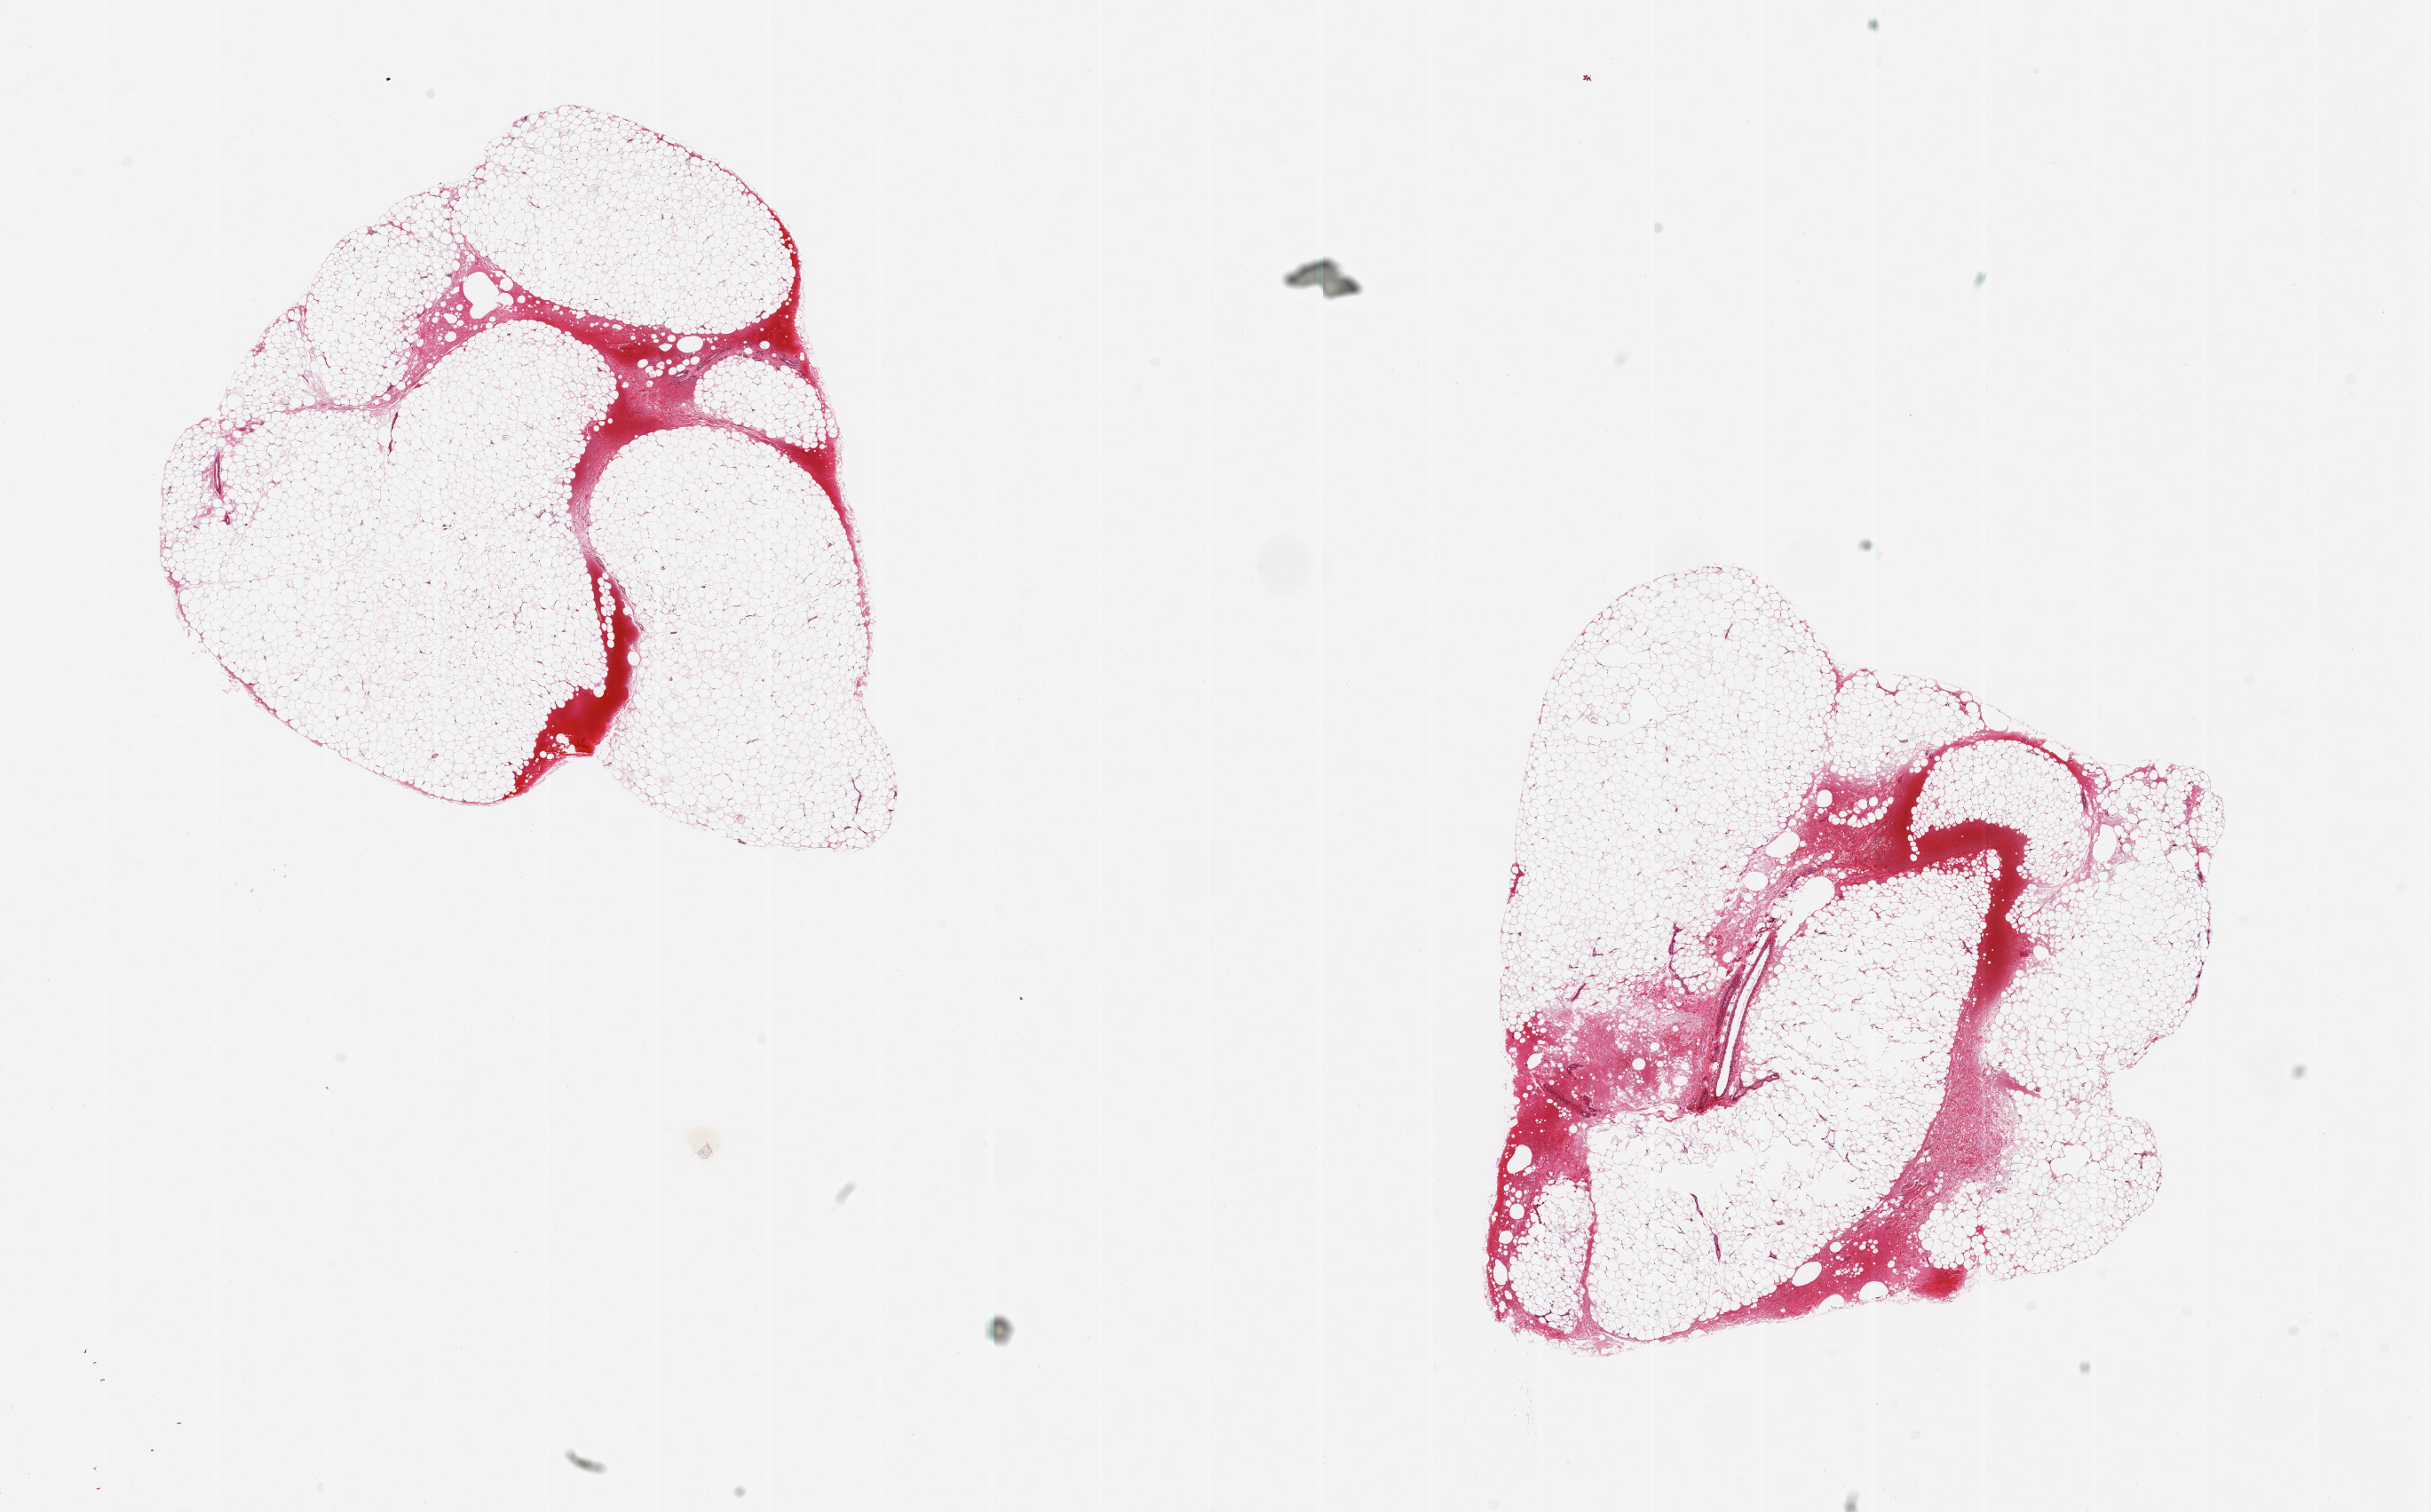
Whole-slide image, haematoxylin and eosin stain, a low-resolution overview of the entire scanned area, about 21.7 x 13.5 mm. PAXgene-fixed, paraffin-embedded tissue. Section of adipose tissue (target tissue). Tissue donor sample.
Pathologist's review note for this sample: 2 pieces, 6x7 & 6x7.5mm ;focal acute hemorrhages, possibly due to trauma.